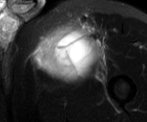
MRI of an extremity soft-tissue mass, one axial slice. Position 46 of 52 along the scan axis. T2-weighted fat-saturated. MR volume resampled by the dataset authors to the PET/CT grid (not the native acquisition matrix). 3.27 mm slice thickness. 147 × 122 image matrix, field of view 144 × 119 mm. Male patient. Case-level facts recorded for this patient, not image findings: histological type: pleiomorphic liposarcoma; grade: high; site of the primary tumour: left thigh.
Structures marked on this image (expert contour drawn on MRI and transferred to this co-registered scan by the dataset authors):
- gross tumour volume including surrounding oedema: bounding box [x1, y1, x2, y2] px = [39, 23, 104, 77]
- gross tumour volume (mass): [39, 32, 88, 74]